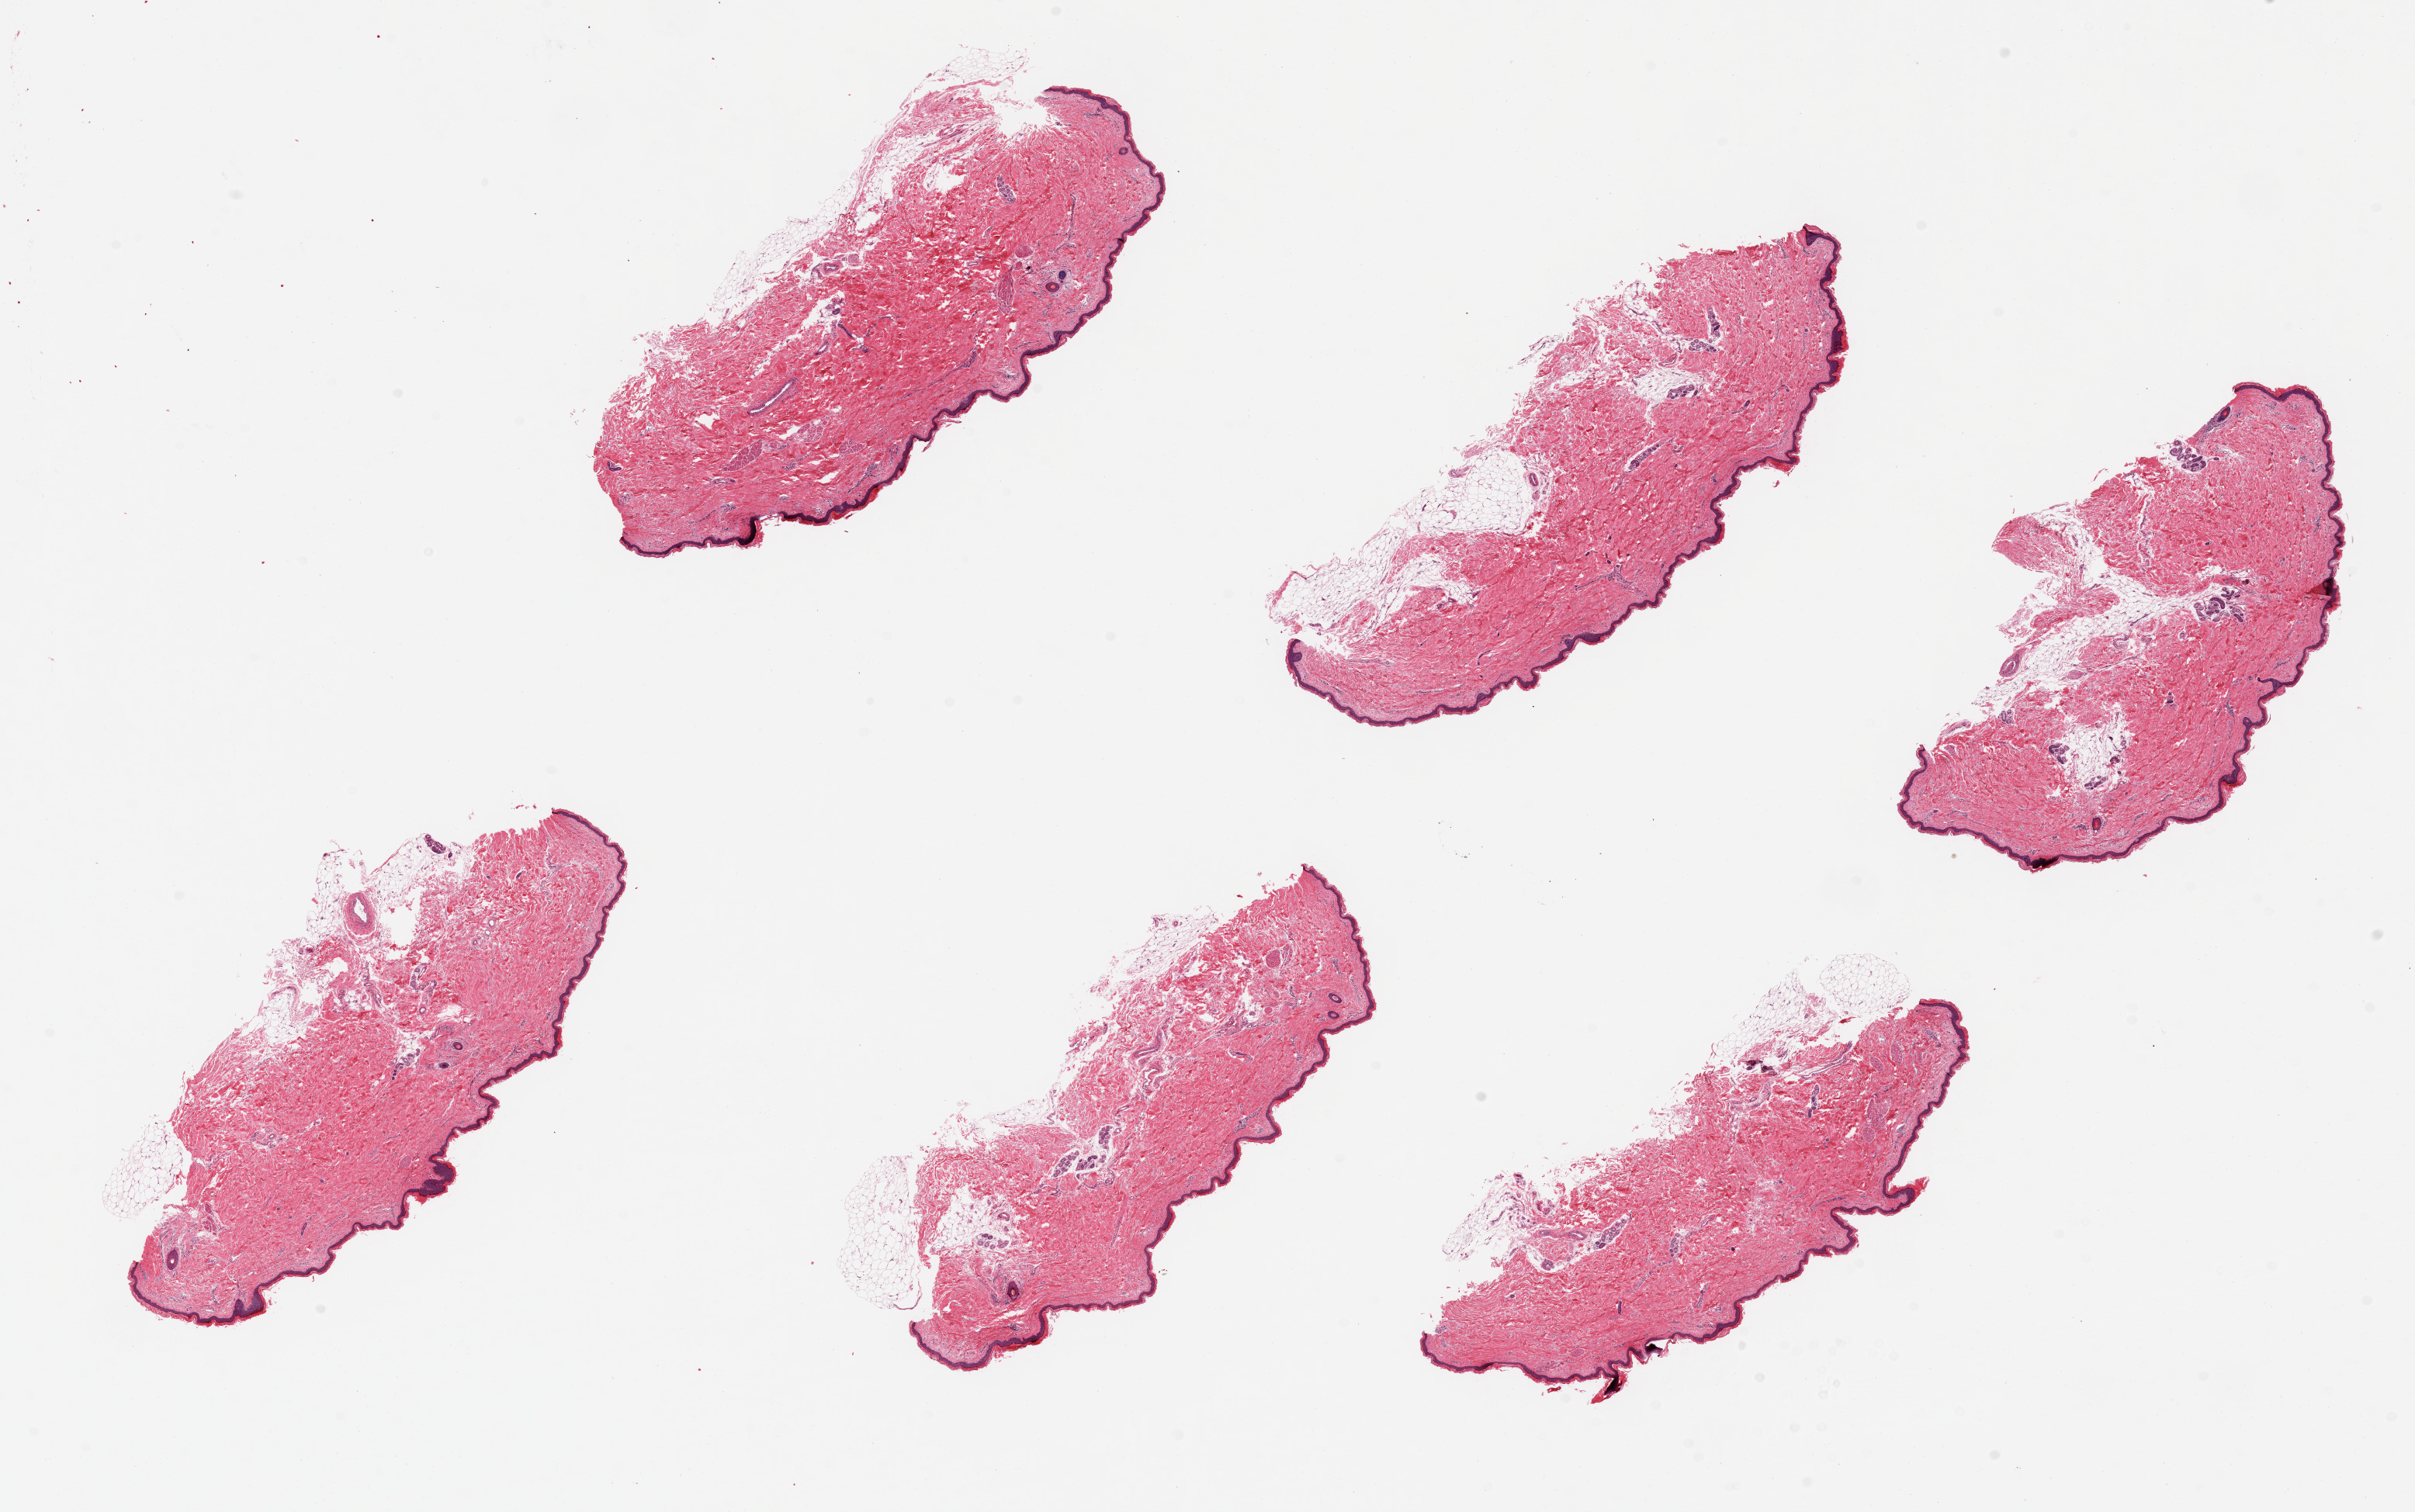
Whole-slide image, H&E stain — low-resolution overview of the scanned area, about 24.6 x 15.4 mm, PAXgene-fixed paraffin-embedded (PFPE) section, section of skin of lower leg (target tissue), donor tissue sample.
- reviewer comment on this tissue sample: 6pieces, 6.5x2.5mm, squamous epithelium is ~1-3% of thickness